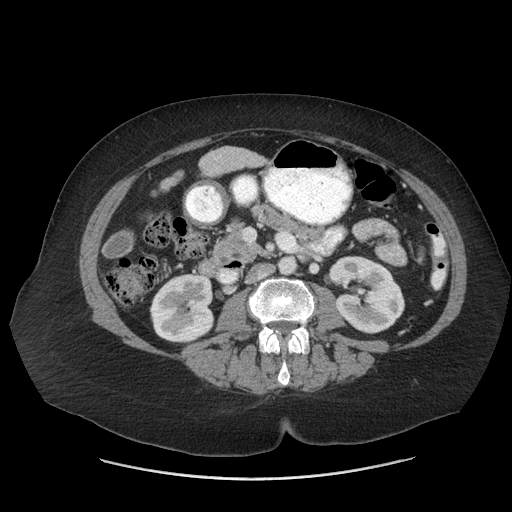
Contrast-enhanced abdominal CT (liver protocol), one axial slice. Slice 13 of 69 in the series (ordered by position). Reconstruction kernel STANDARD. 140 kVp. Soft-tissue window (W 400 / L 40 HU). 2.5 mm slice thickness. 512 × 512 image matrix, field of view 420 × 420 mm. Case-level facts recorded for this patient, not image findings: diagnosis: hepatocellular carcinoma (patient treated with transarterial chemoembolisation; whether this scan precedes or follows treatment is not stated here); TNM stage (as recorded): Stage-IIIB.
Structures marked on this image (semi-automatic segmentation, software-assisted and operator-edited):
- liver parenchyma outside the tumour (the mass and vessels are separate outlines, so this box may not span the whole liver): bounding box [x1, y1, x2, y2] px = [245, 154, 254, 164]